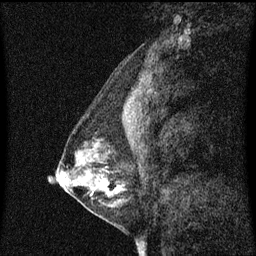
Breast MRI (dynamic contrast-enhanced), one sagittal slice. Slice 22 of 60 in the series (ordered by position). Dynamic contrast-enhanced series, image 2 of 3 at this slice position (ordered by acquisition). 1.5 T. TE 4.2 ms, TR 8.4 ms. 256 × 256 image matrix. Female patient, age 41 years. From the clinical record (not read from this slice): setting: breast cancer imaged before/during neoadjuvant chemotherapy; receptor status: triple-negative.
Annotated regions visible in this slice (semi-automatic segmentation, software-assisted and operator-edited):
- analysis volume of interest (the breast-tissue region the enhancement analysis was run in; not a lesion): bounding box [x1, y1, x2, y2] px = [64, 124, 135, 209]
- tumour enhancement mask (voxels above the 70 % enhancement threshold inside the analysis volume of interest): [108, 192, 117, 195]